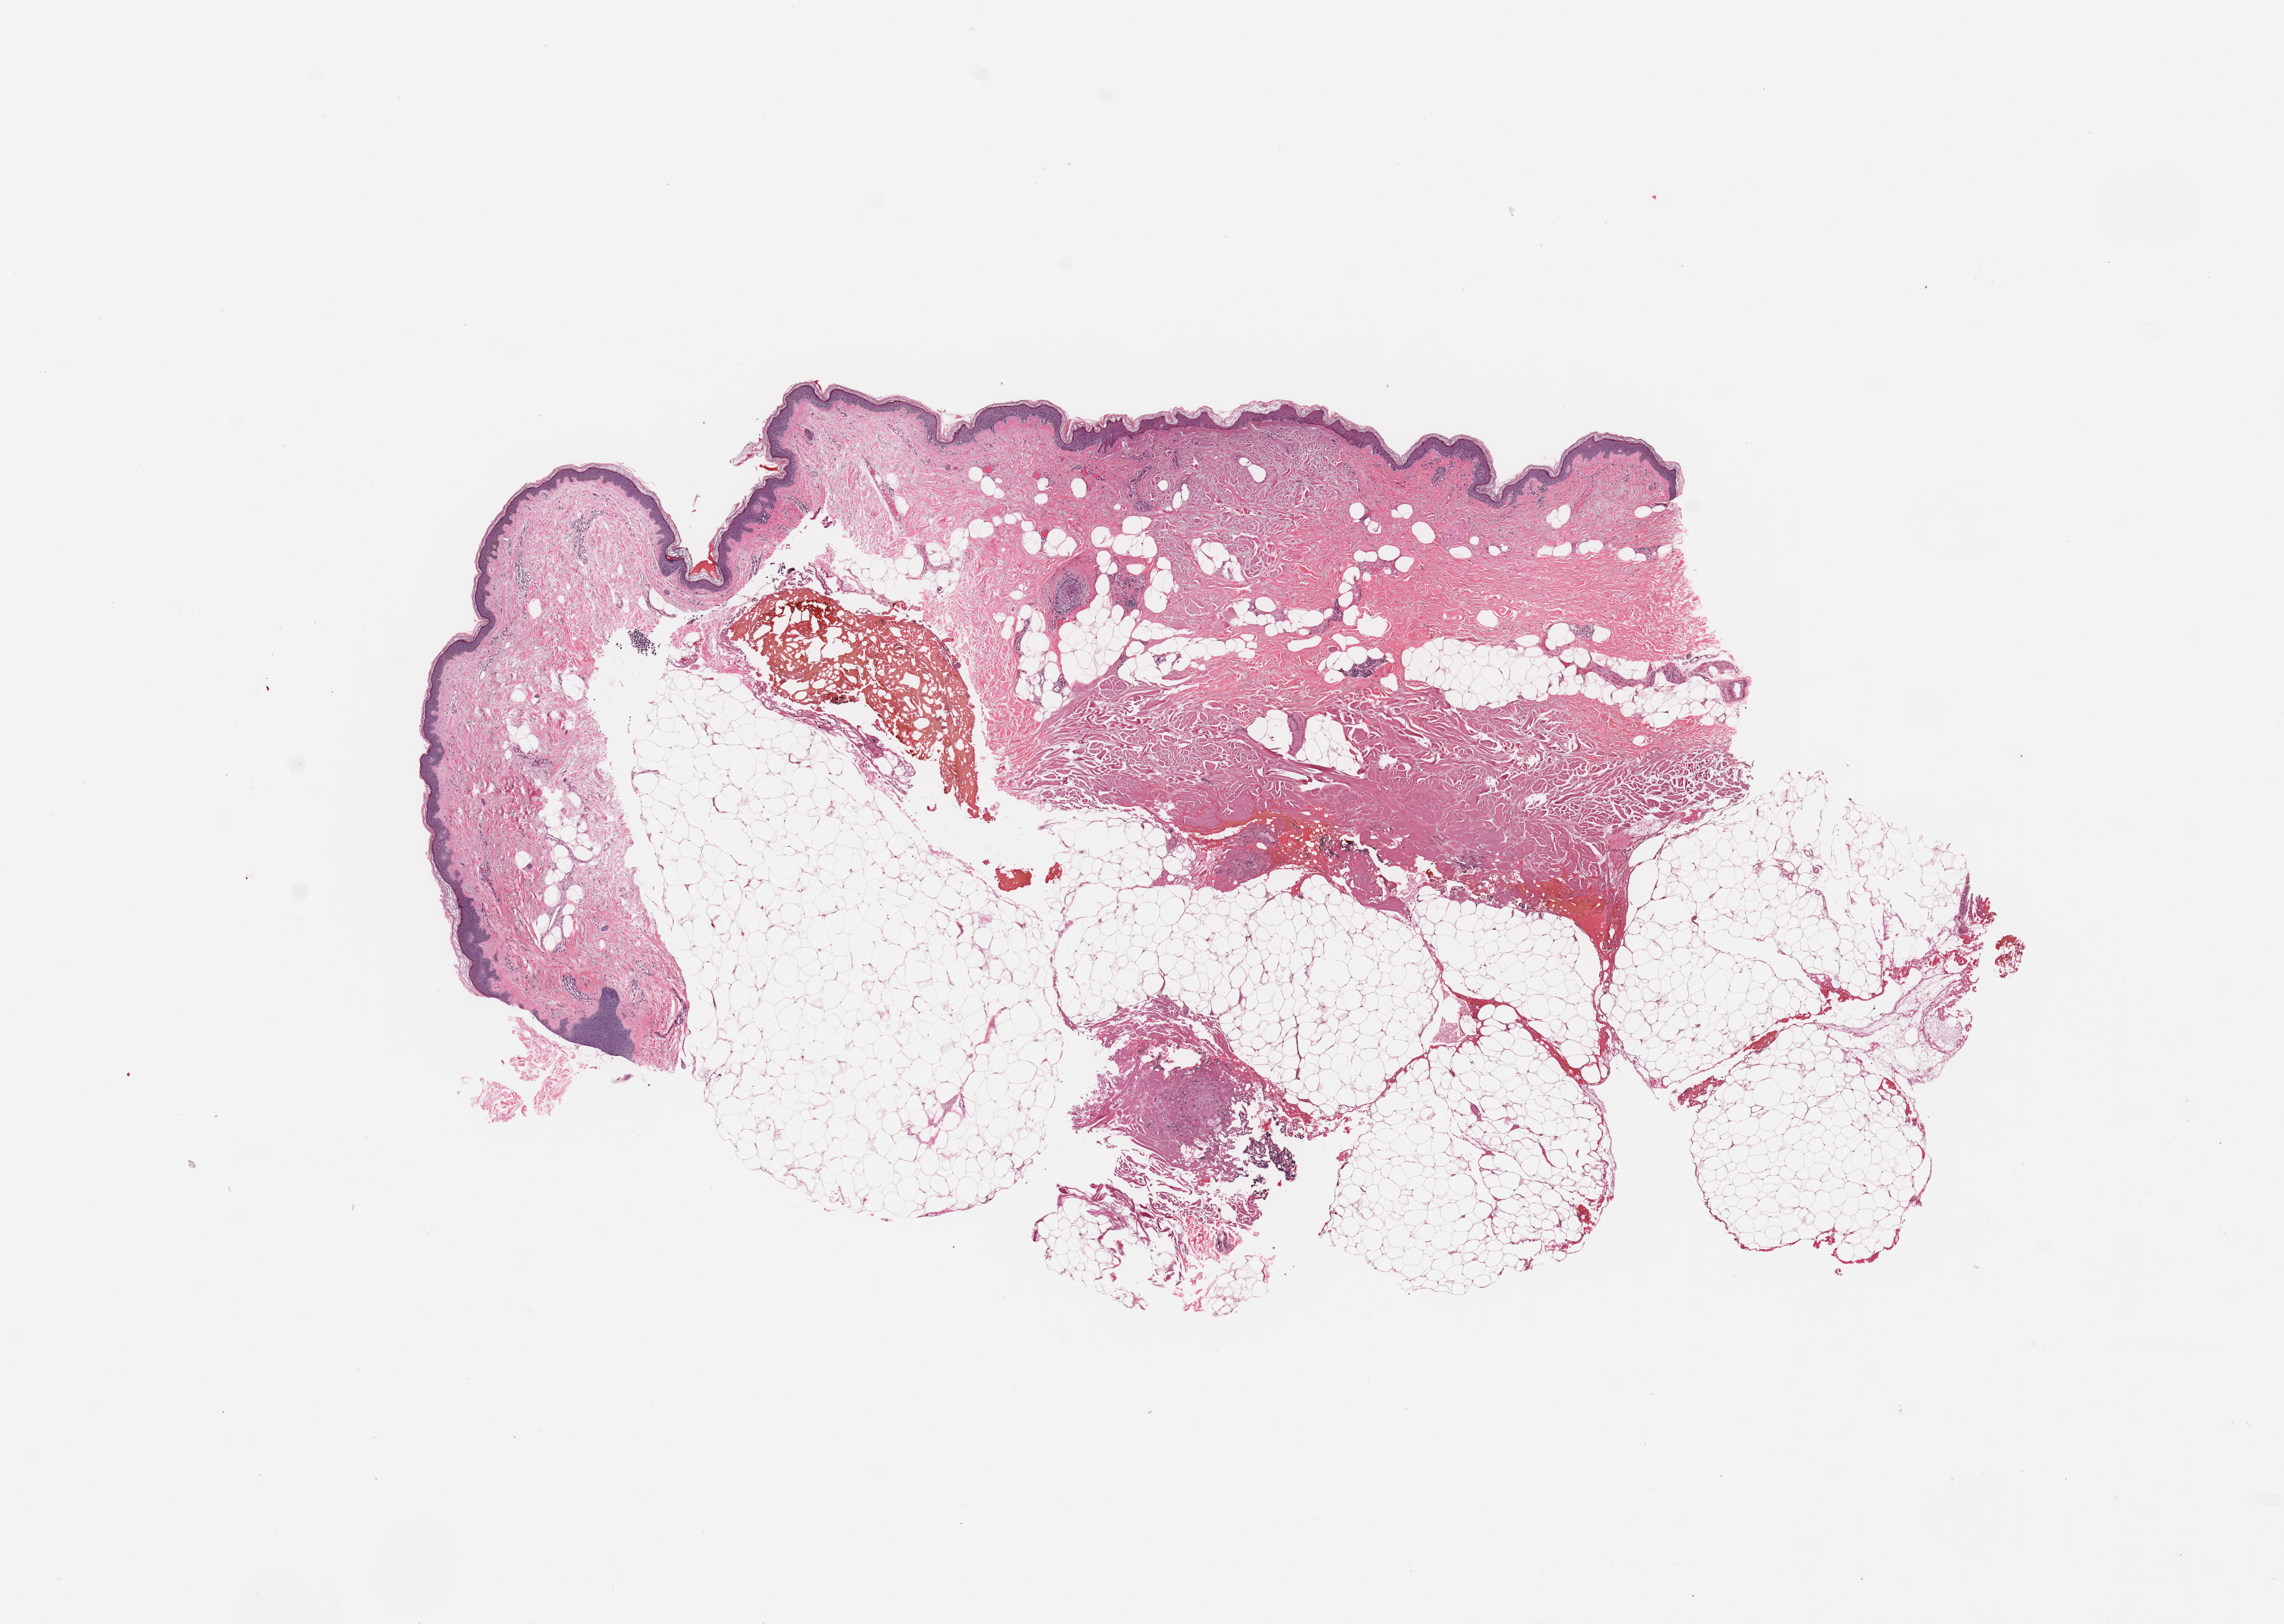
H&E-stained whole-slide image, a low-resolution overview of the entire scanned area, about 13.8 x 9.8 mm (from a 20x scan), normal (non-tumour) tissue sample, sampled site: skin. 73-year-old female patient.
This section: normal (non-tumour) tissue from the same patient. Patient diagnosis: Malignant melanoma, NOS.